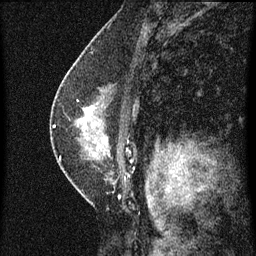
Breast MRI (dynamic contrast-enhanced), one sagittal slice; position 38 of 60 along the scan axis; dynamic contrast-enhanced series, image 2 of 3 at this slice position (ordered by acquisition); 1.5 T; TE 4.2 ms, TR 8 ms; 256 × 256 image matrix. Patient: female, 47 years.
Structures marked on this image (semi-automatically segmented with operator editing):
- analysis volume of interest (the breast-tissue region the enhancement analysis was run in; not a lesion): bounding box (x1, y1, x2, y2) in pixels: (54, 80, 137, 187)
- tumour enhancement mask (voxels above the 70 % enhancement threshold inside the analysis volume of interest): (54, 126, 132, 161)